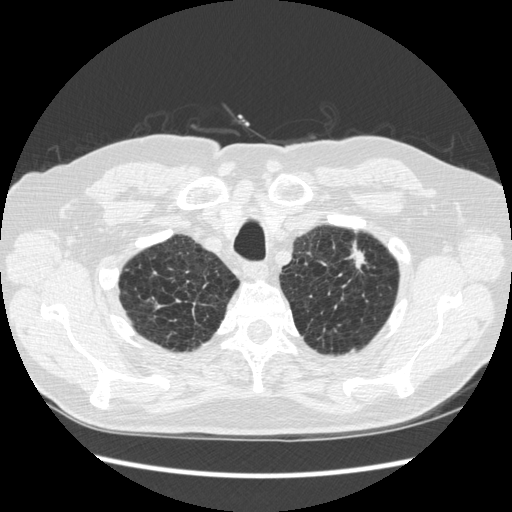
Low-dose screening chest CT, one axial slice; slice 236 of 267 in the series (ordered by position); reconstruction kernel STANDARD; 120 kVp; lung window (W 1500 / L -600 HU); 1.25 mm slice thickness; 512 × 512 image matrix, field of view 360 × 360 mm.
Annotated regions visible in this slice (manually delineated by an expert):
- lesion 1 (tumor, upper lobe of left lung): bounding box [x1, y1, x2, y2] px = [349, 242, 366, 269]